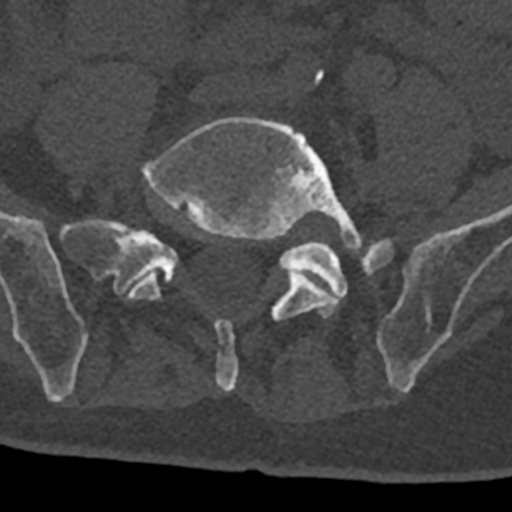
CT including the spine, one axial slice; reconstruction kernel Br40s/3; bone window (W 1800 / L 400 HU); 512 × 512 image matrix, field of view 160 × 160 mm. Male patient, age 74 years. From the clinical record (not read from this slice): primary cancer: renal.
Structures marked on this image (semi-automatically segmented with operator editing):
- L4 vertebra: box from (x=314, y=70) to (x=324, y=85) px
- L5 vertebra: (x=127, y=116)–(x=362, y=392)